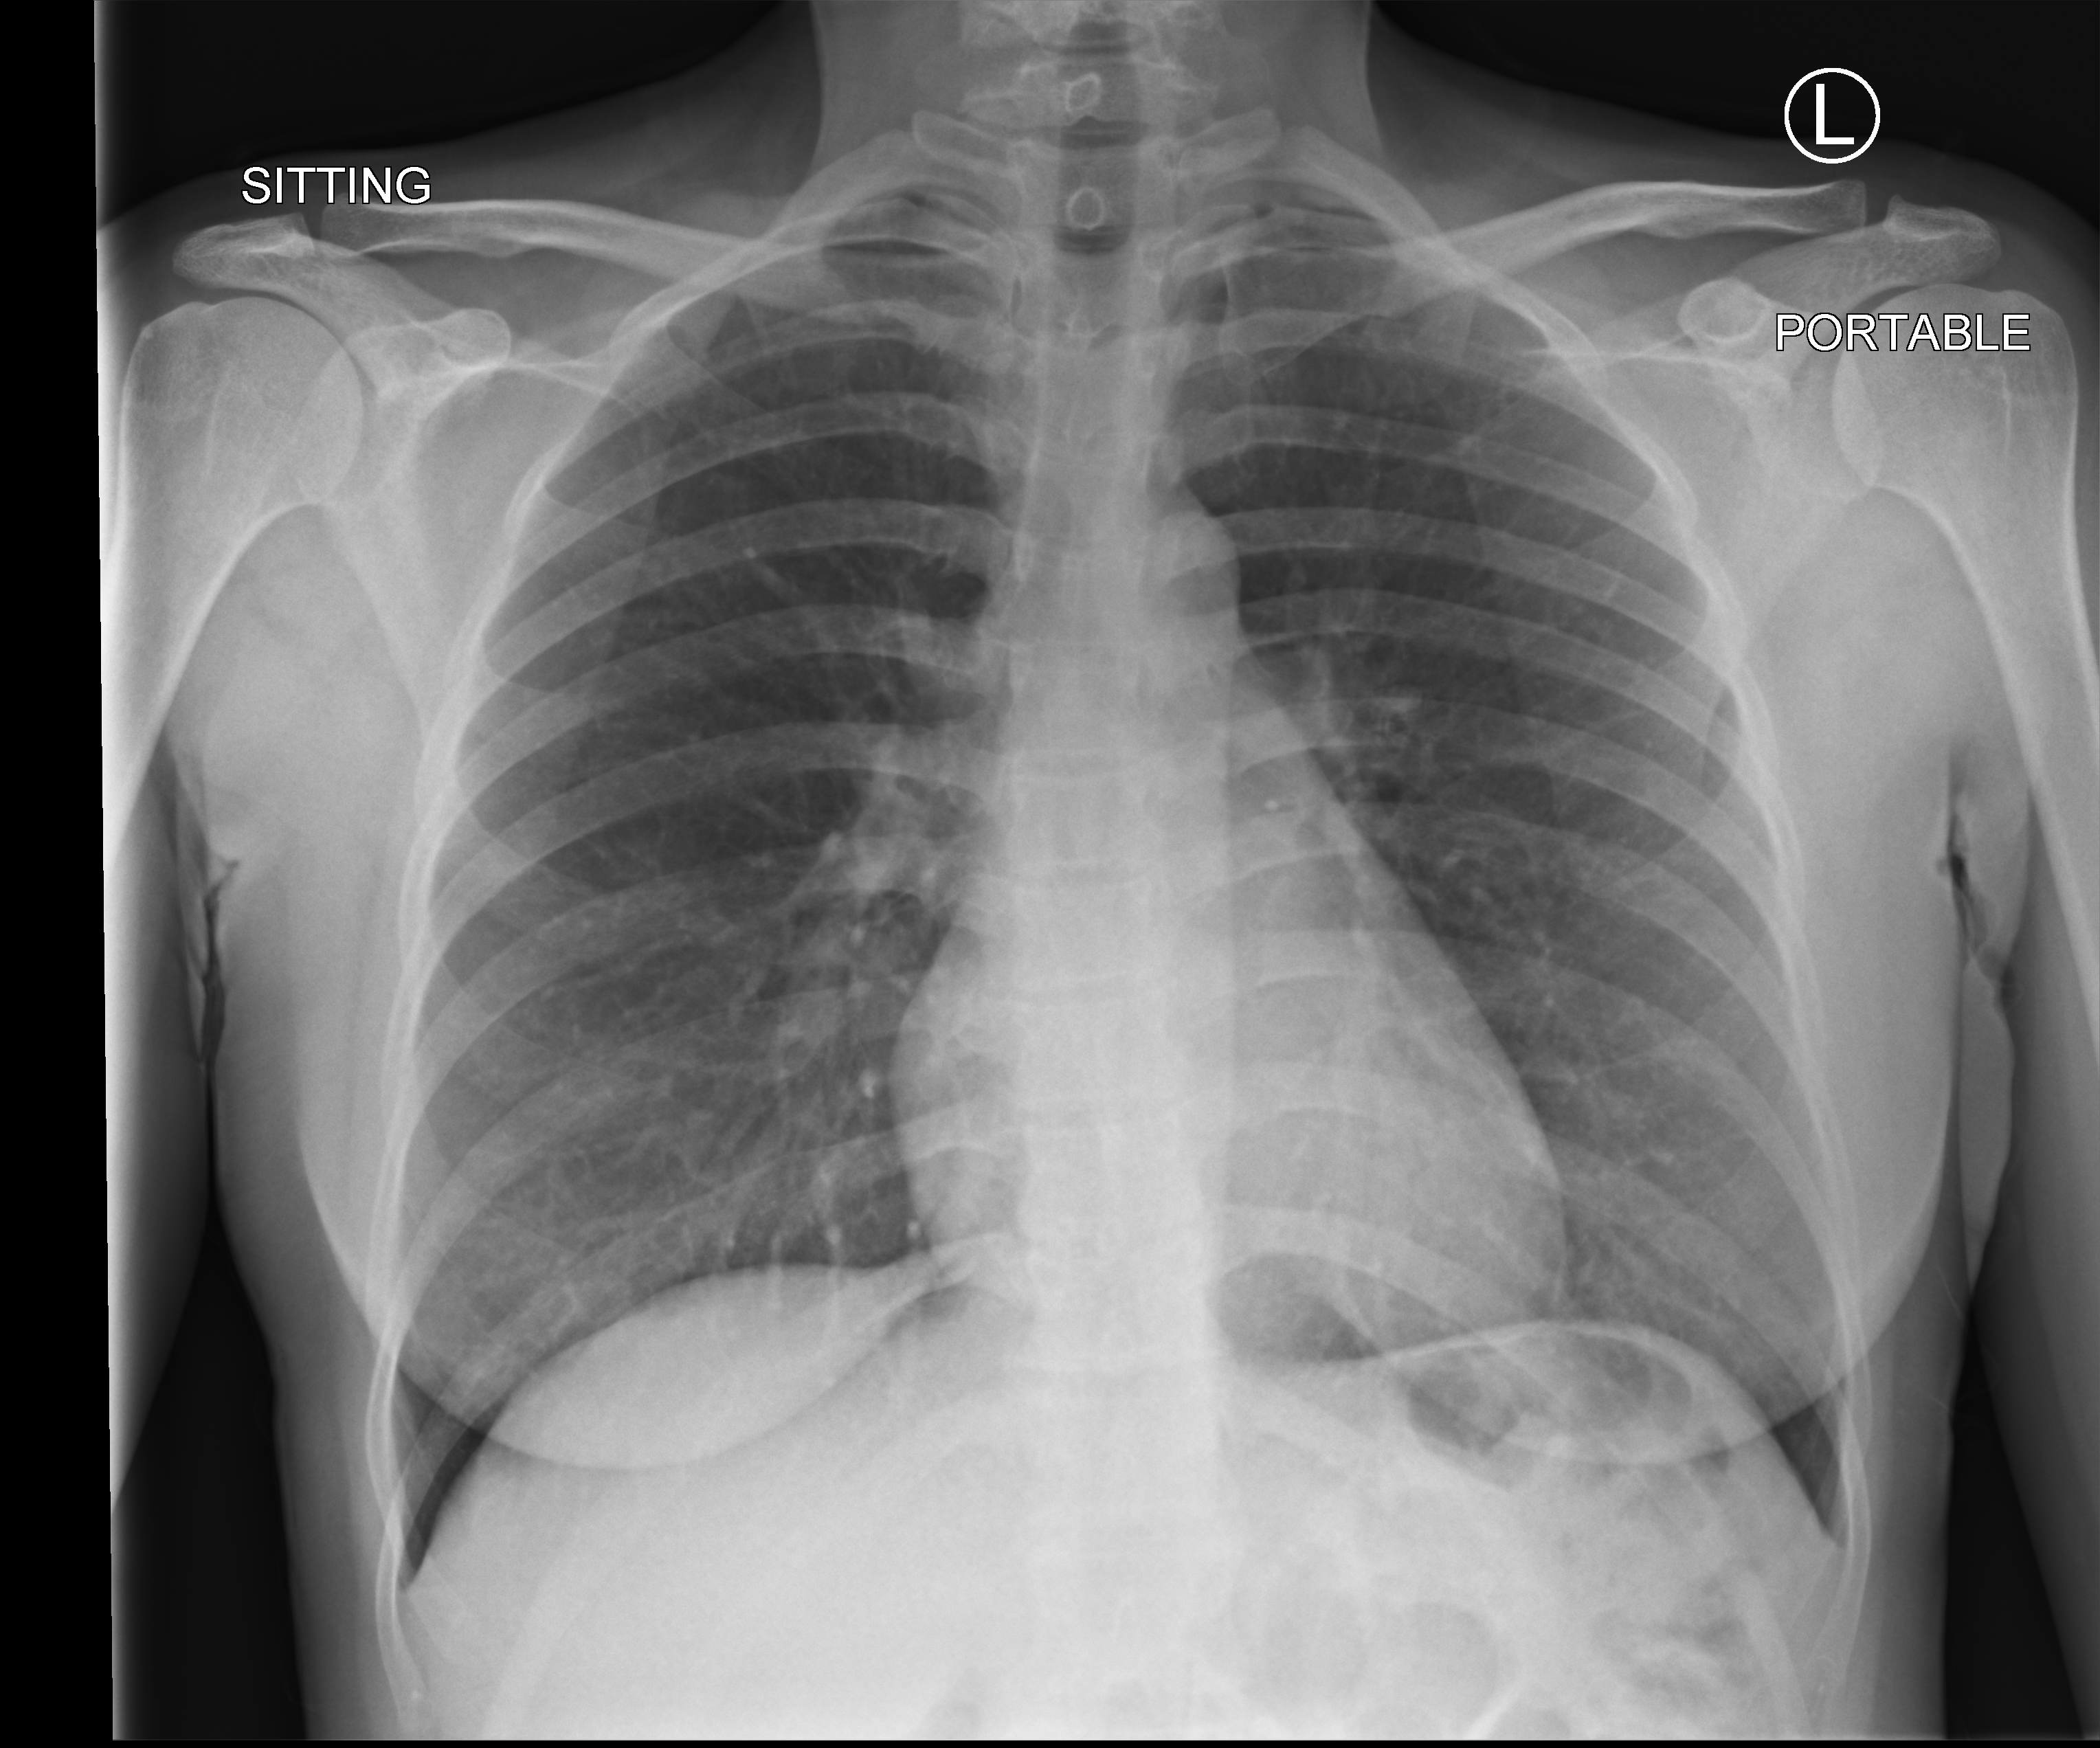
Bedside chest radiograph (computed radiography). Female patient hospitalised with COVID-19, age 18–59 years.
From the hospital-stay record, not from the radiograph (when in the stay this image was taken is not recorded):
- diabetes (admission record): no
- length of hospital stay: 1 day
- admitted to intensive care during this hospital stay: no